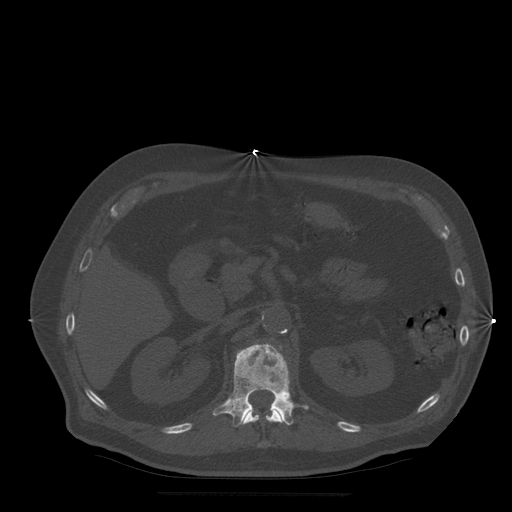
CT including the spine, one axial slice; position 202 of 522 along the scan axis; bone window (W 1800 / L 400 HU); 1.25 mm slice thickness; 512 × 512 image matrix. Patient age 72 years. From the clinical record (not read from this slice): primary cancer: prostate.
Outlined on this slice (semi-automatic segmentation, software-assisted and operator-edited):
- L1 vertebra: box from (x=213, y=344) to (x=309, y=427) px
- T12 vertebra: (x=243, y=408)–(x=283, y=447)